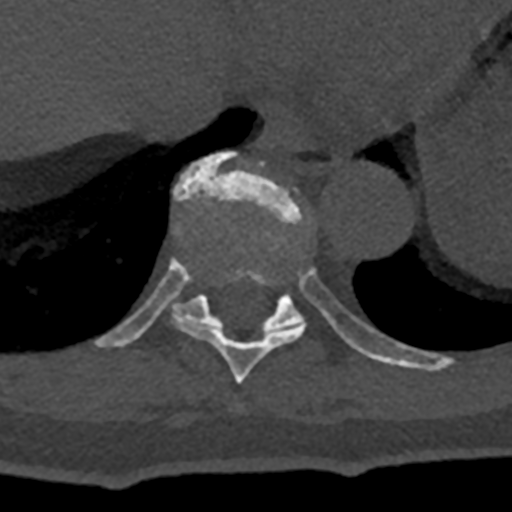
CT including the spine, one axial slice. Position 633 of 797 along the scan axis. Reconstruction kernel Br40s/3. 120 kVp. Bone window (W 1800 / L 400 HU). 0.5 mm slice thickness. 512 × 512 image matrix, field of view 160 × 160 mm. Male patient, age 74 years. From the clinical record (not read from this slice): primary cancer: renal.
Structures marked on this image (semi-automatic segmentation, software-assisted and operator-edited):
- T10 vertebra: box from (x=94, y=151) to (x=432, y=371) px
- T9 vertebra: (x=171, y=258)–(x=305, y=384)